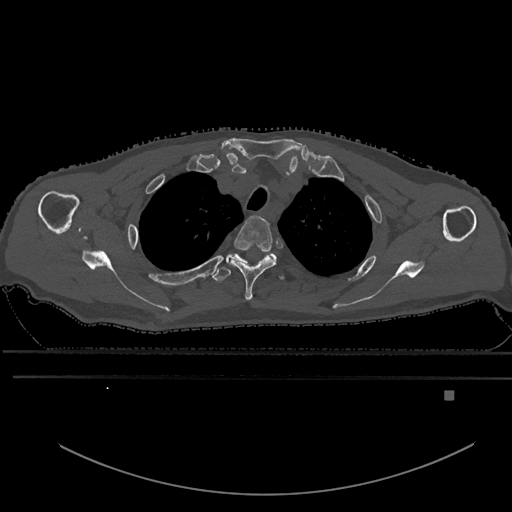
CT including the spine, one axial slice. Position 483 of 969 along the scan axis. Bone window (W 1800 / L 400 HU). 0.5 mm slice thickness. 512 × 512 image matrix, field of view 456 × 456 mm. Patient: male, 82 years. Case-level facts recorded for this patient, not image findings: primary cancer: prostate.
Annotated regions visible in this slice (semi-automatically segmented with operator editing):
- T2 vertebra: bounding box <227,215,277,301> (left, top, right, bottom; pixels)
- T3 vertebra: <212,254,286,282>